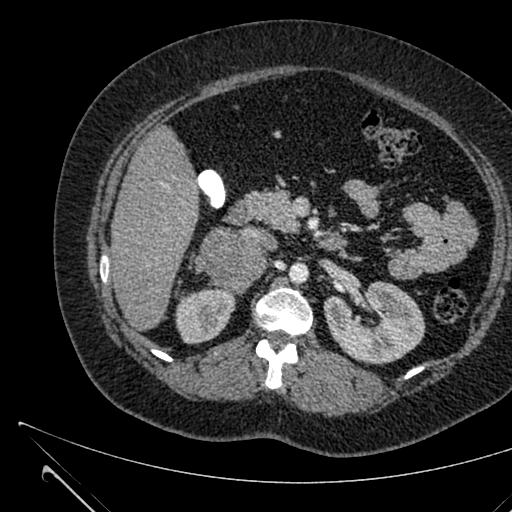
Contrast-enhanced abdominal CT, one axial slice. Slice 368 of 731 in the series (ordered by position). Intravenous contrast given. Soft-tissue window (W 400 / L 40 HU). 1 mm slice thickness. 512 × 512 image matrix, field of view 376 × 376 mm. Female patient, age 36 years. From the clinical record (not read from this slice): diagnosis: adrenocortical carcinoma; tumour side: right adrenal; tumour size at pathology: 10 cm; Ki-67 index: 20 %; stage (as recorded): 4.
Structures marked on this image (semi-automatic segmentation, software-assisted and operator-edited):
- mass: bounding box (x1, y1, x2, y2) in pixels: (202, 229, 265, 291)